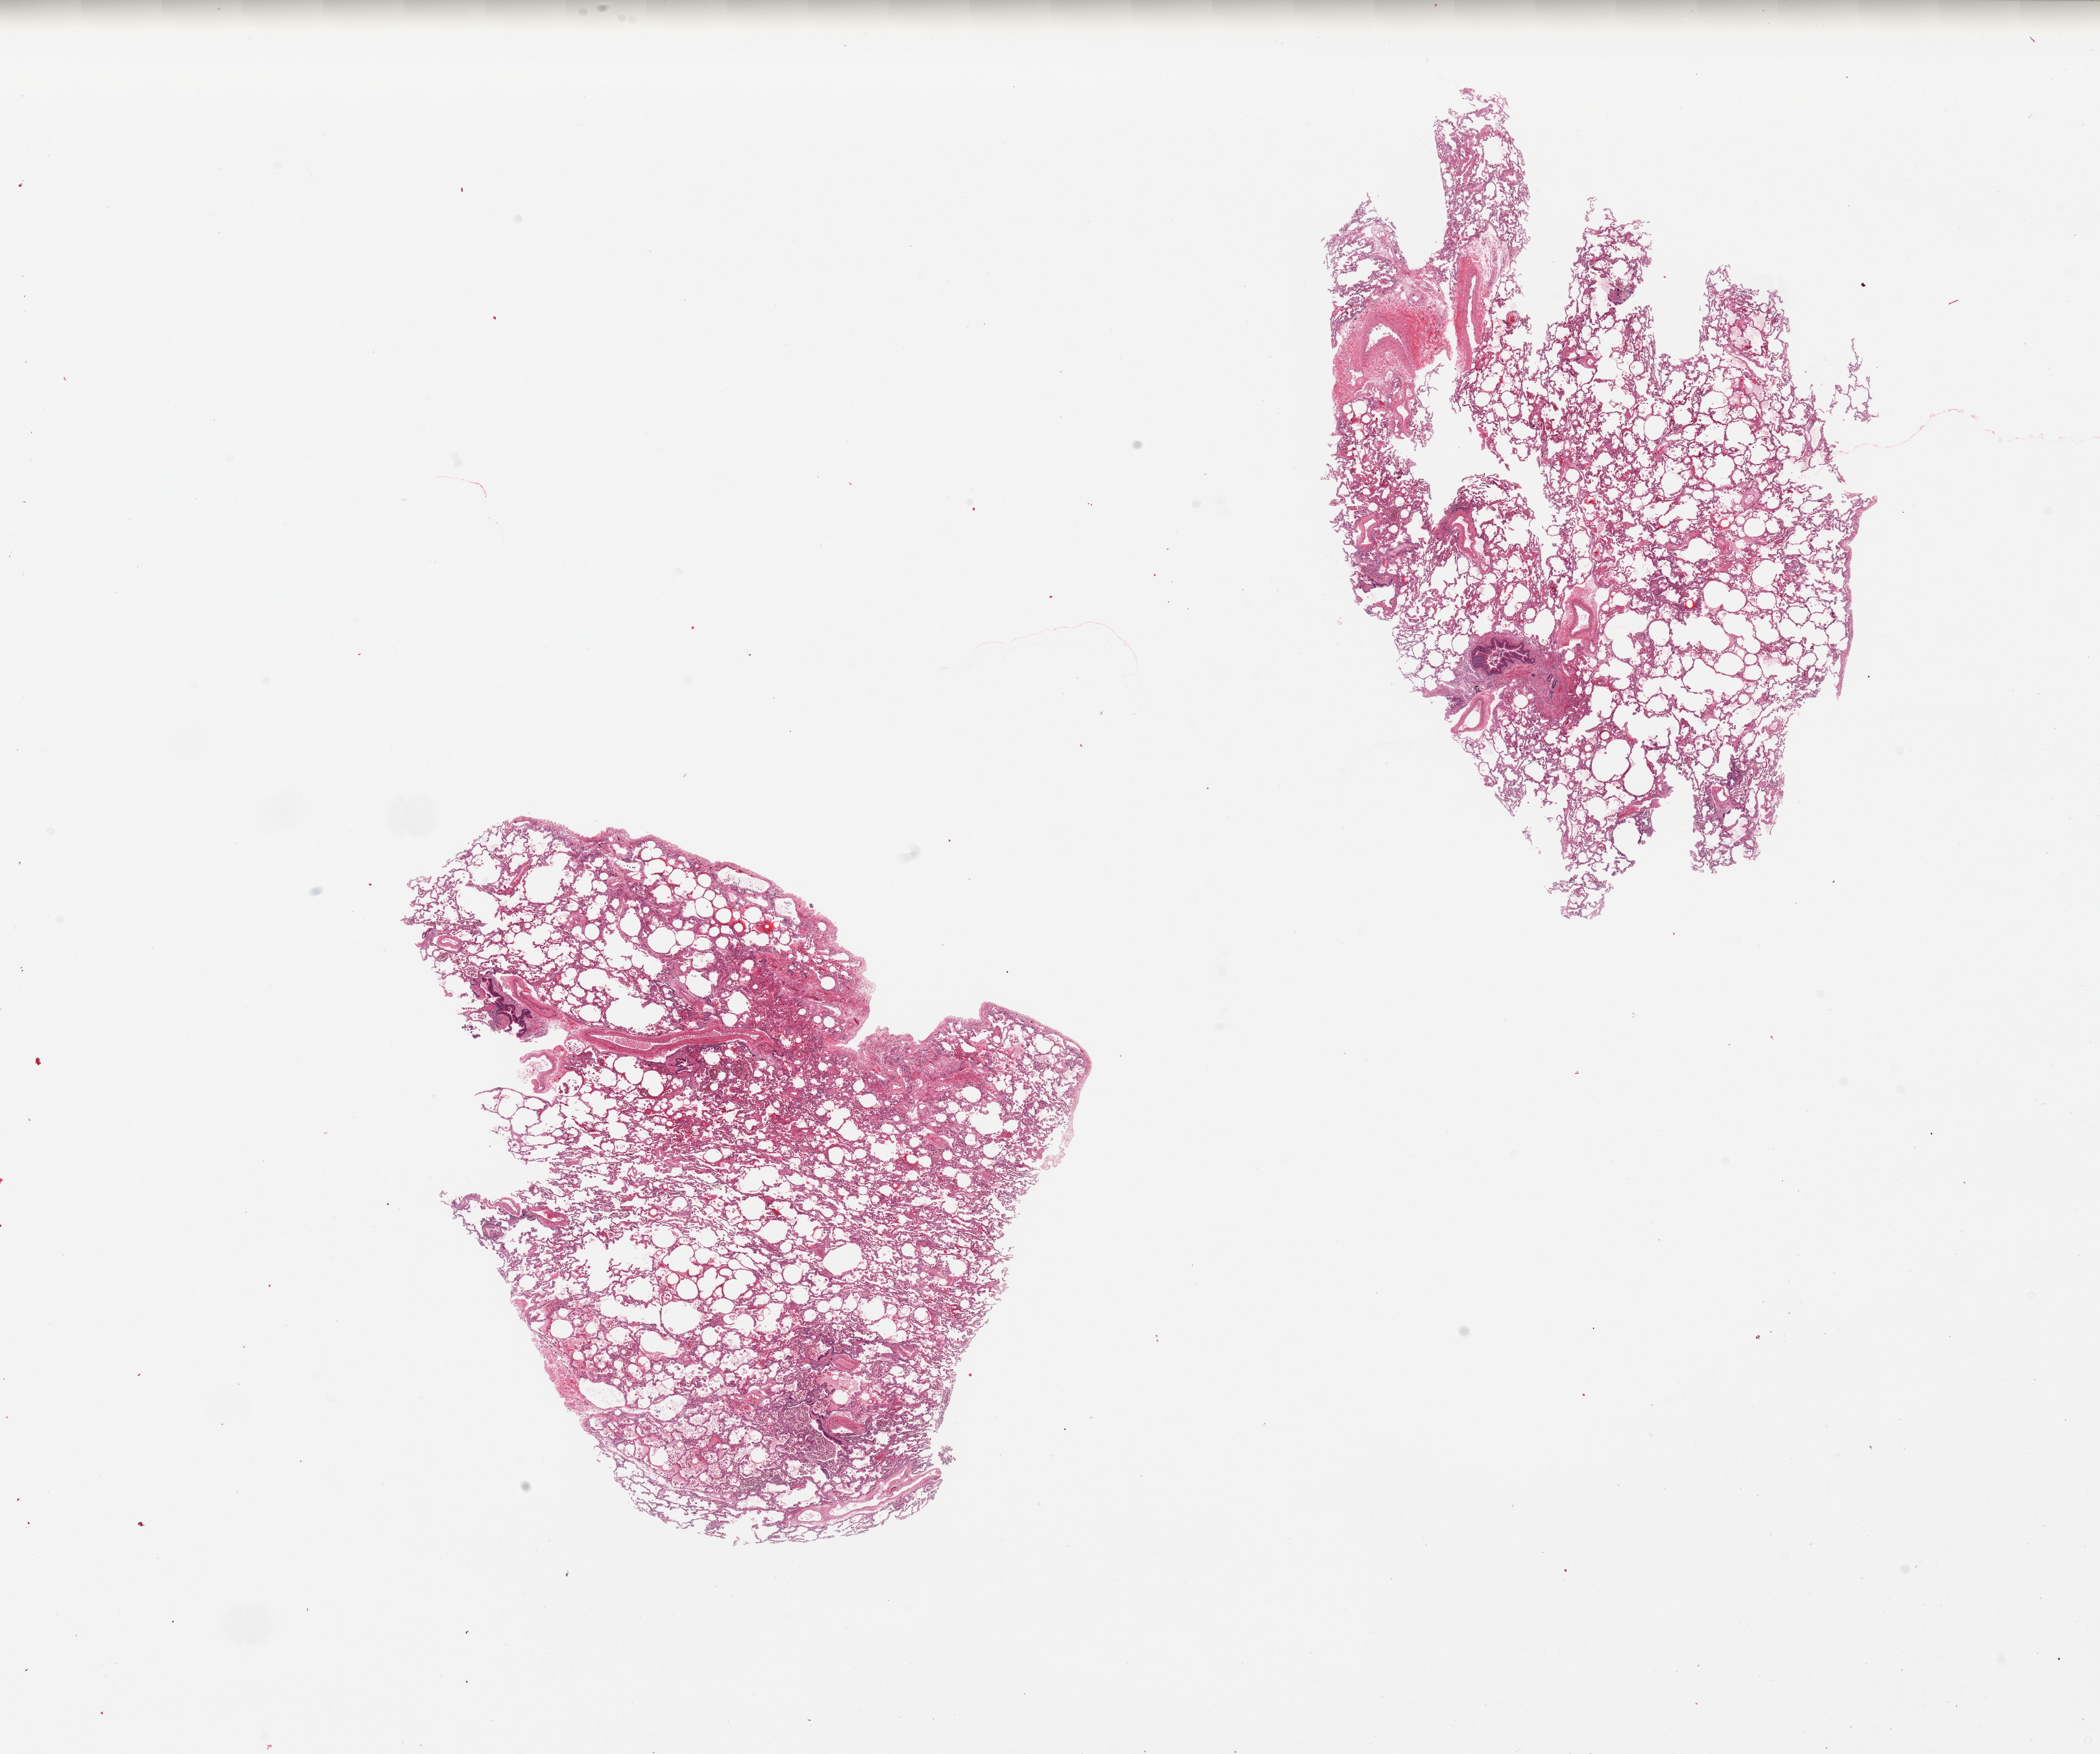
Whole-slide image, haematoxylin and eosin stain — low-resolution overview of the scanned area, about 25.6 x 21.4 mm (slide scanned at 20x); PAXgene-fixed paraffin-embedded (PFPE) section; target tissue: lung; donor tissue sample. Female donor.
* pathologist's review note for this sample: 2 pieces patchy mild/moderate congestion with hemosiderin laden macrophages prominenet